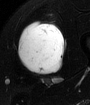
MRI of an extremity soft-tissue mass, one axial slice; slice 36 of 65 in the series (ordered by position); T2-weighted fat-saturated; MR volume resampled by the dataset authors to the PET/CT grid (not the native acquisition matrix); 90 × 105 image matrix, field of view 88 × 103 mm. Male patient. From the clinical record (not read from this slice): histological type: mixoid liposarcoma; grade: low; site of the primary tumour: left thigh.
Outlined on this slice (expert contour drawn on MRI and transferred to this co-registered scan by the dataset authors):
- gross tumour volume (mass): bounding box (x1, y1, x2, y2) in pixels: (16, 21, 65, 76)